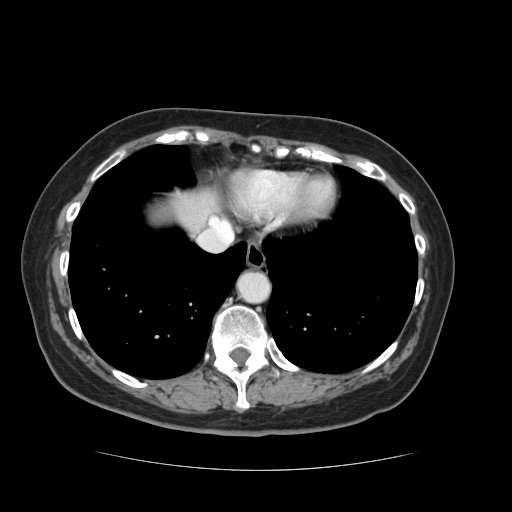
Contrast-enhanced abdominal CT, one axial slice. Slice 116 of 128 in the series (ordered by position). Intravenous contrast given. Soft-tissue window (W 400 / L 40 HU). 2.5 mm slice thickness. 512 × 512 image matrix, field of view 366 × 366 mm. Female patient, age 67 years. From the clinical record (not read from this slice): diagnosis: colorectal cancer liver metastases, imaged before liver resection; multiple liver metastases: yes; largest metastasis: 3 cm; disease in both lobes: yes.
Outlined on this slice (manually delineated by an expert):
- liver: bounding box (x1, y1, x2, y2) in pixels: (156, 189, 213, 231)
- planned liver remnant (the part of the liver to remain after resection): (172, 197, 212, 233)